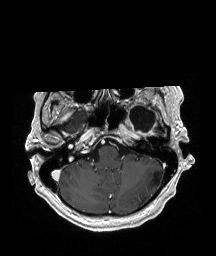
Brain MRI from a brain-tumour surgery series, one axial slice. T1-weighted post-contrast. 1 mm slice thickness. 216 × 256 image matrix, field of view 211 × 250 mm. From the clinical record (not read from this slice): histopathology: Glioblastoma; WHO grade: 4.
Annotated regions visible in this slice (expert manual segmentation):
- previous resection cavity: bounding box (x1, y1, x2, y2) in pixels: (128, 106, 155, 132)